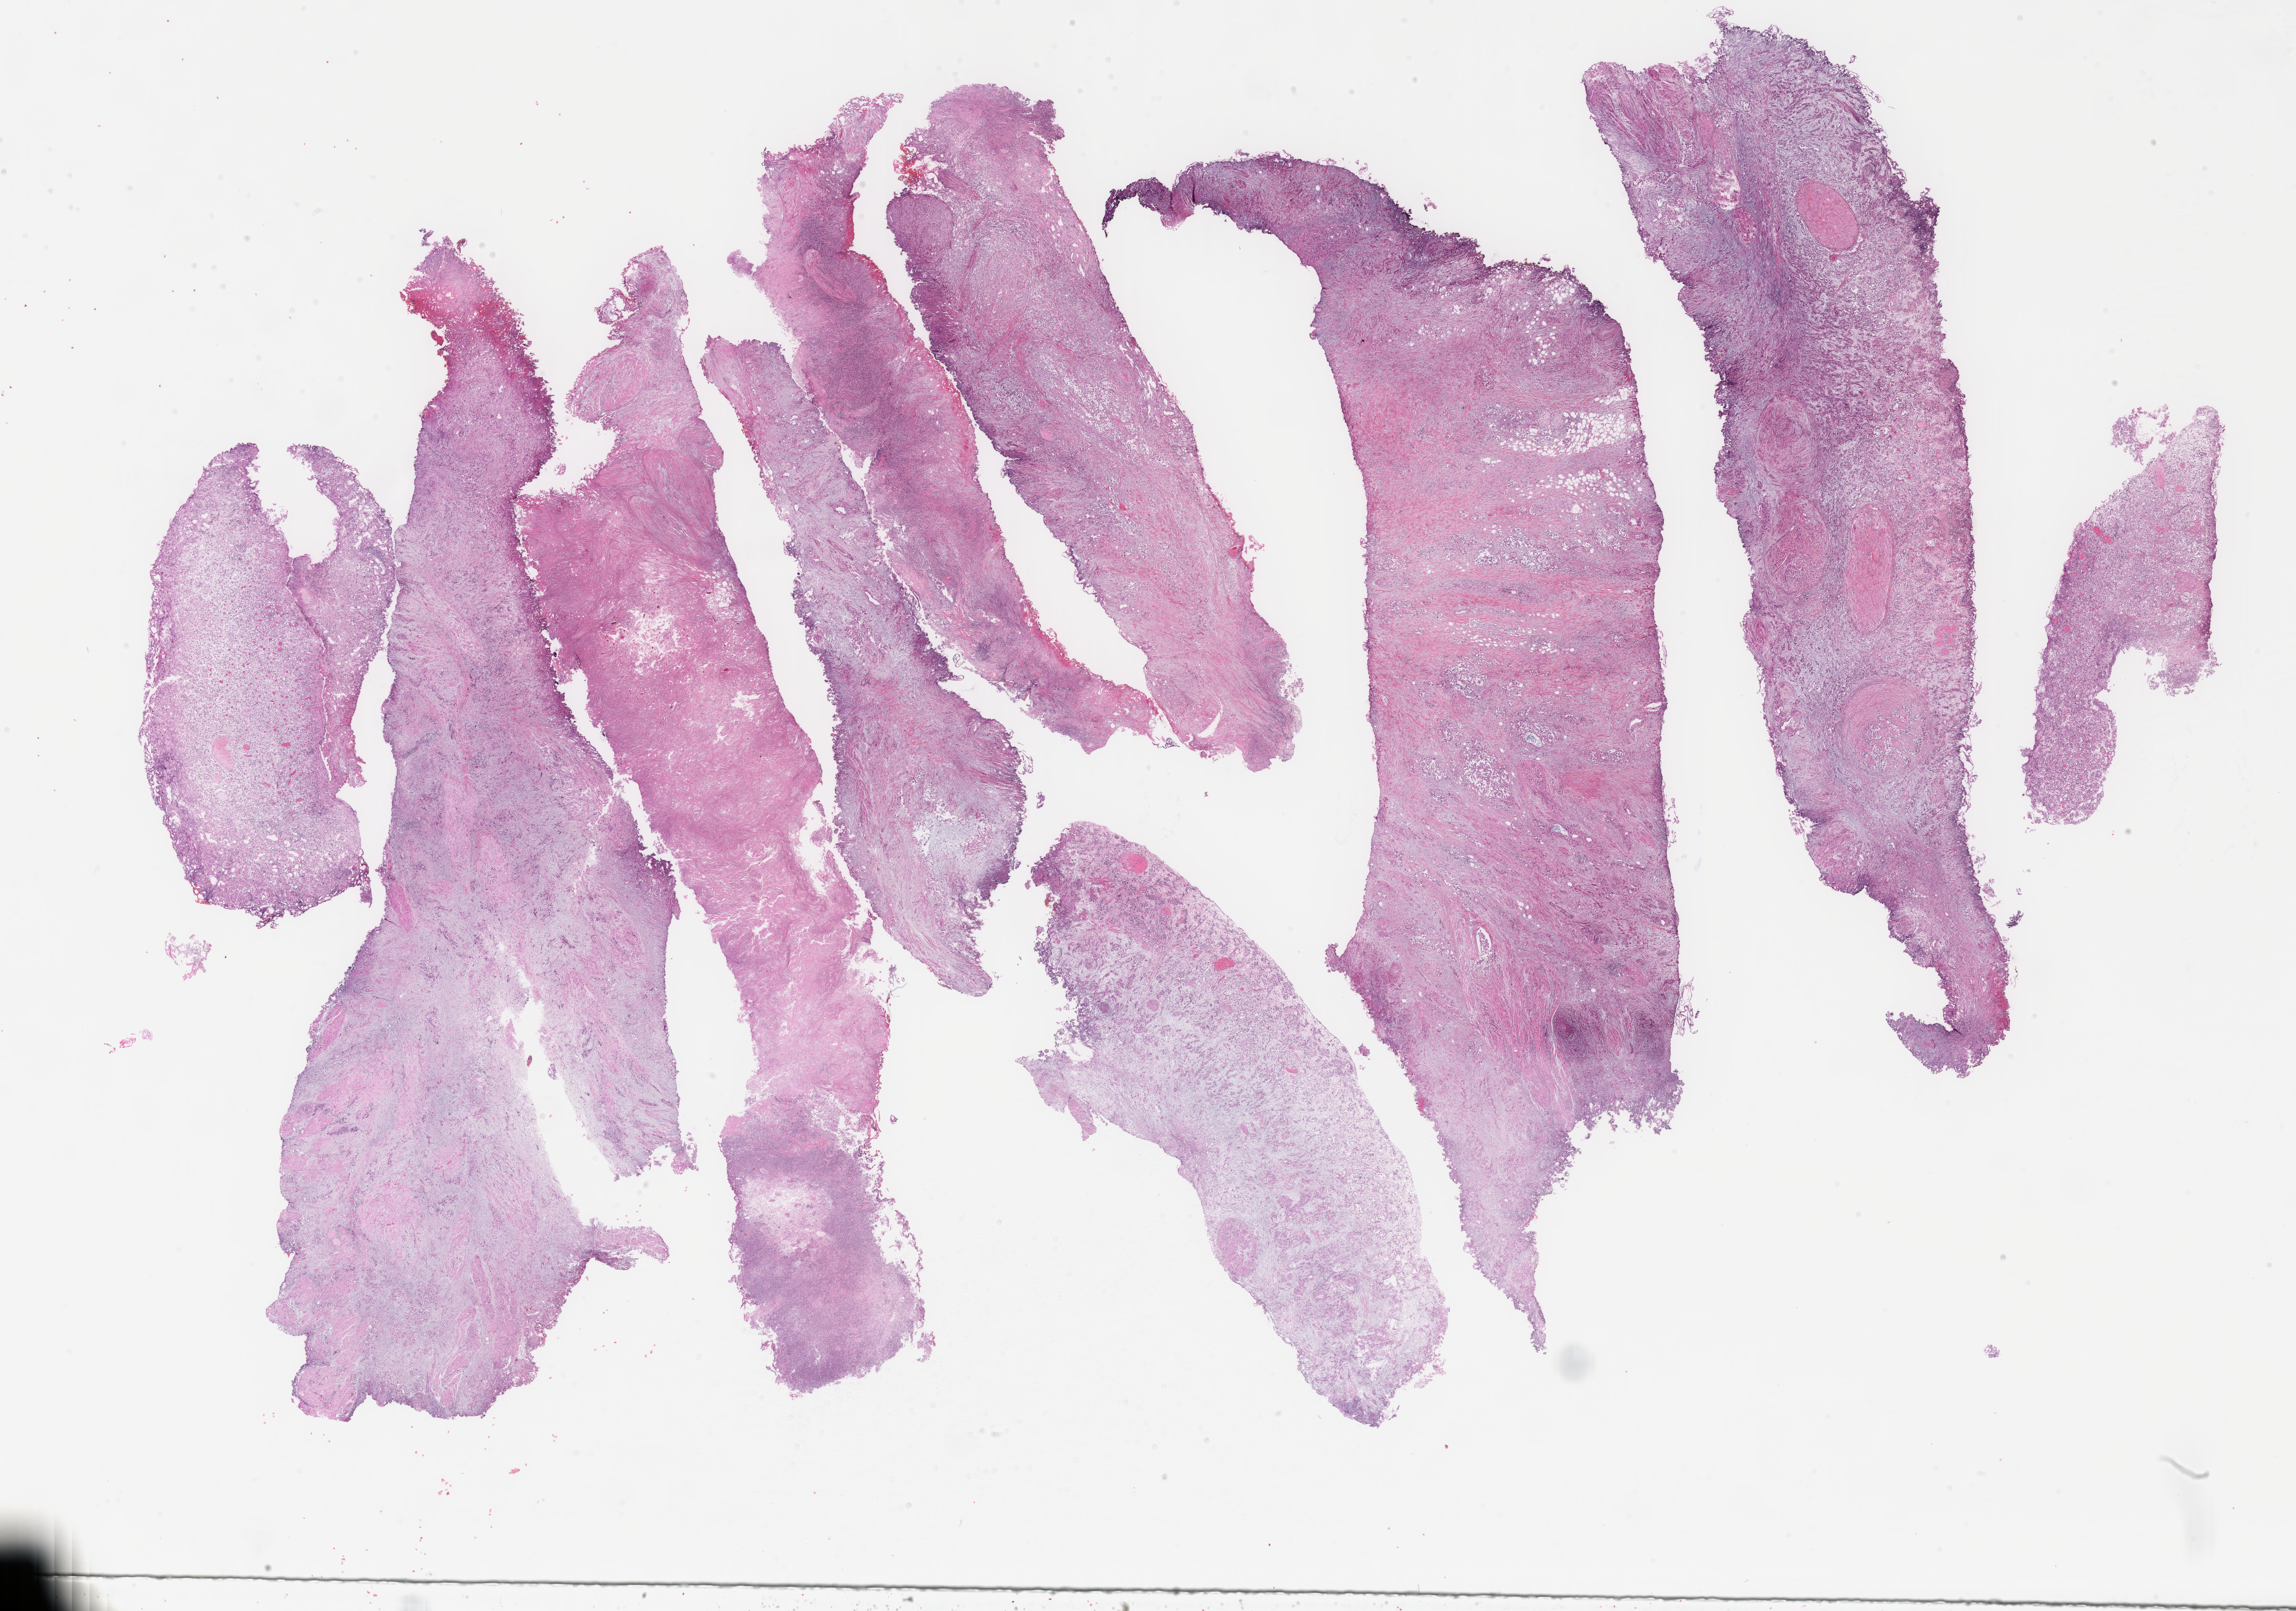
H&E-stained whole-slide image — low-resolution overview of the scanned area, about 30.7 x 21.5 mm (acquisition: 40x scan); formalin-fixed paraffin-embedded (FFPE) diagnostic section; primary tumour sample from the bladder. Female, age 58 years at initial diagnosis. Histologic grade: high grade.
Pathologic diagnosis: Transitional cell carcinoma. AJCC pathologic stage: II.